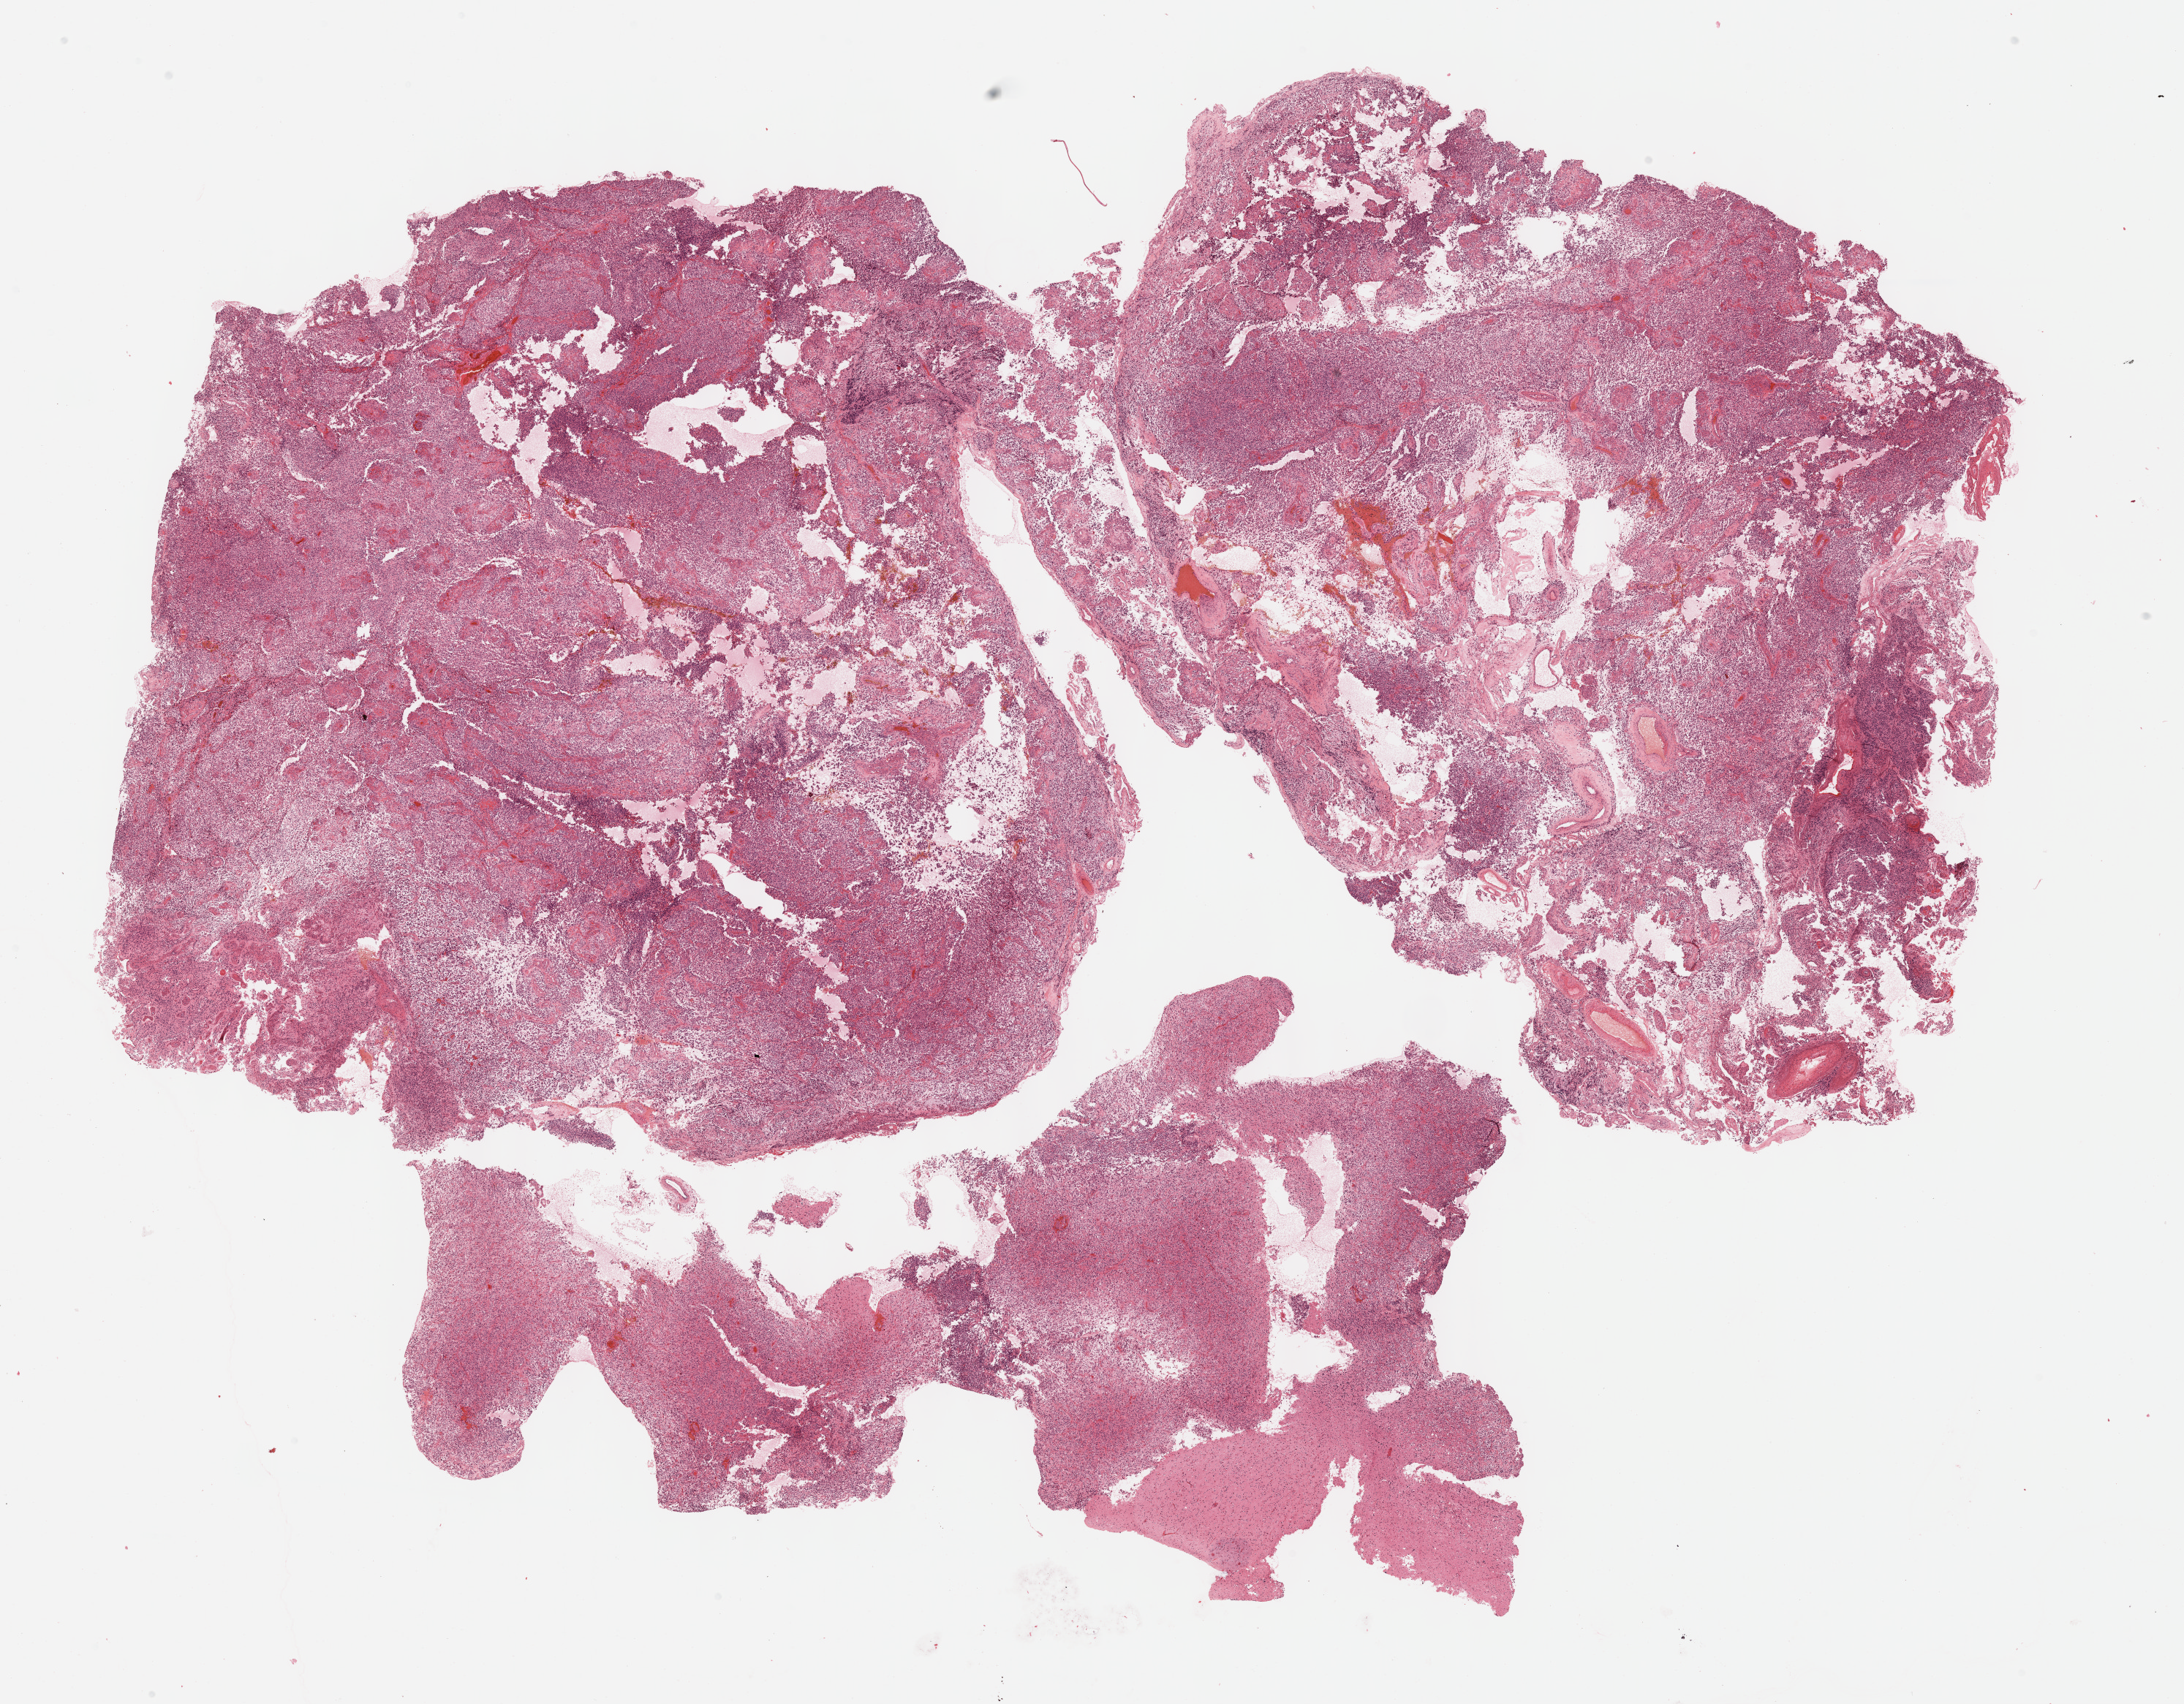
Whole-slide histology image, Hematoxylin and eosin (H&E) stained, shown as a low-resolution overview of the whole scanned area (about 24.2 x 18.9 mm, from a 40x scan). FFPE section. Primary tumour sample from the brain. Male patient; age at initial diagnosis 63 years. Histologic grade: G3 (poorly differentiated).
- diagnosis: Oligodendroglioma, anaplastic (cerebrum)